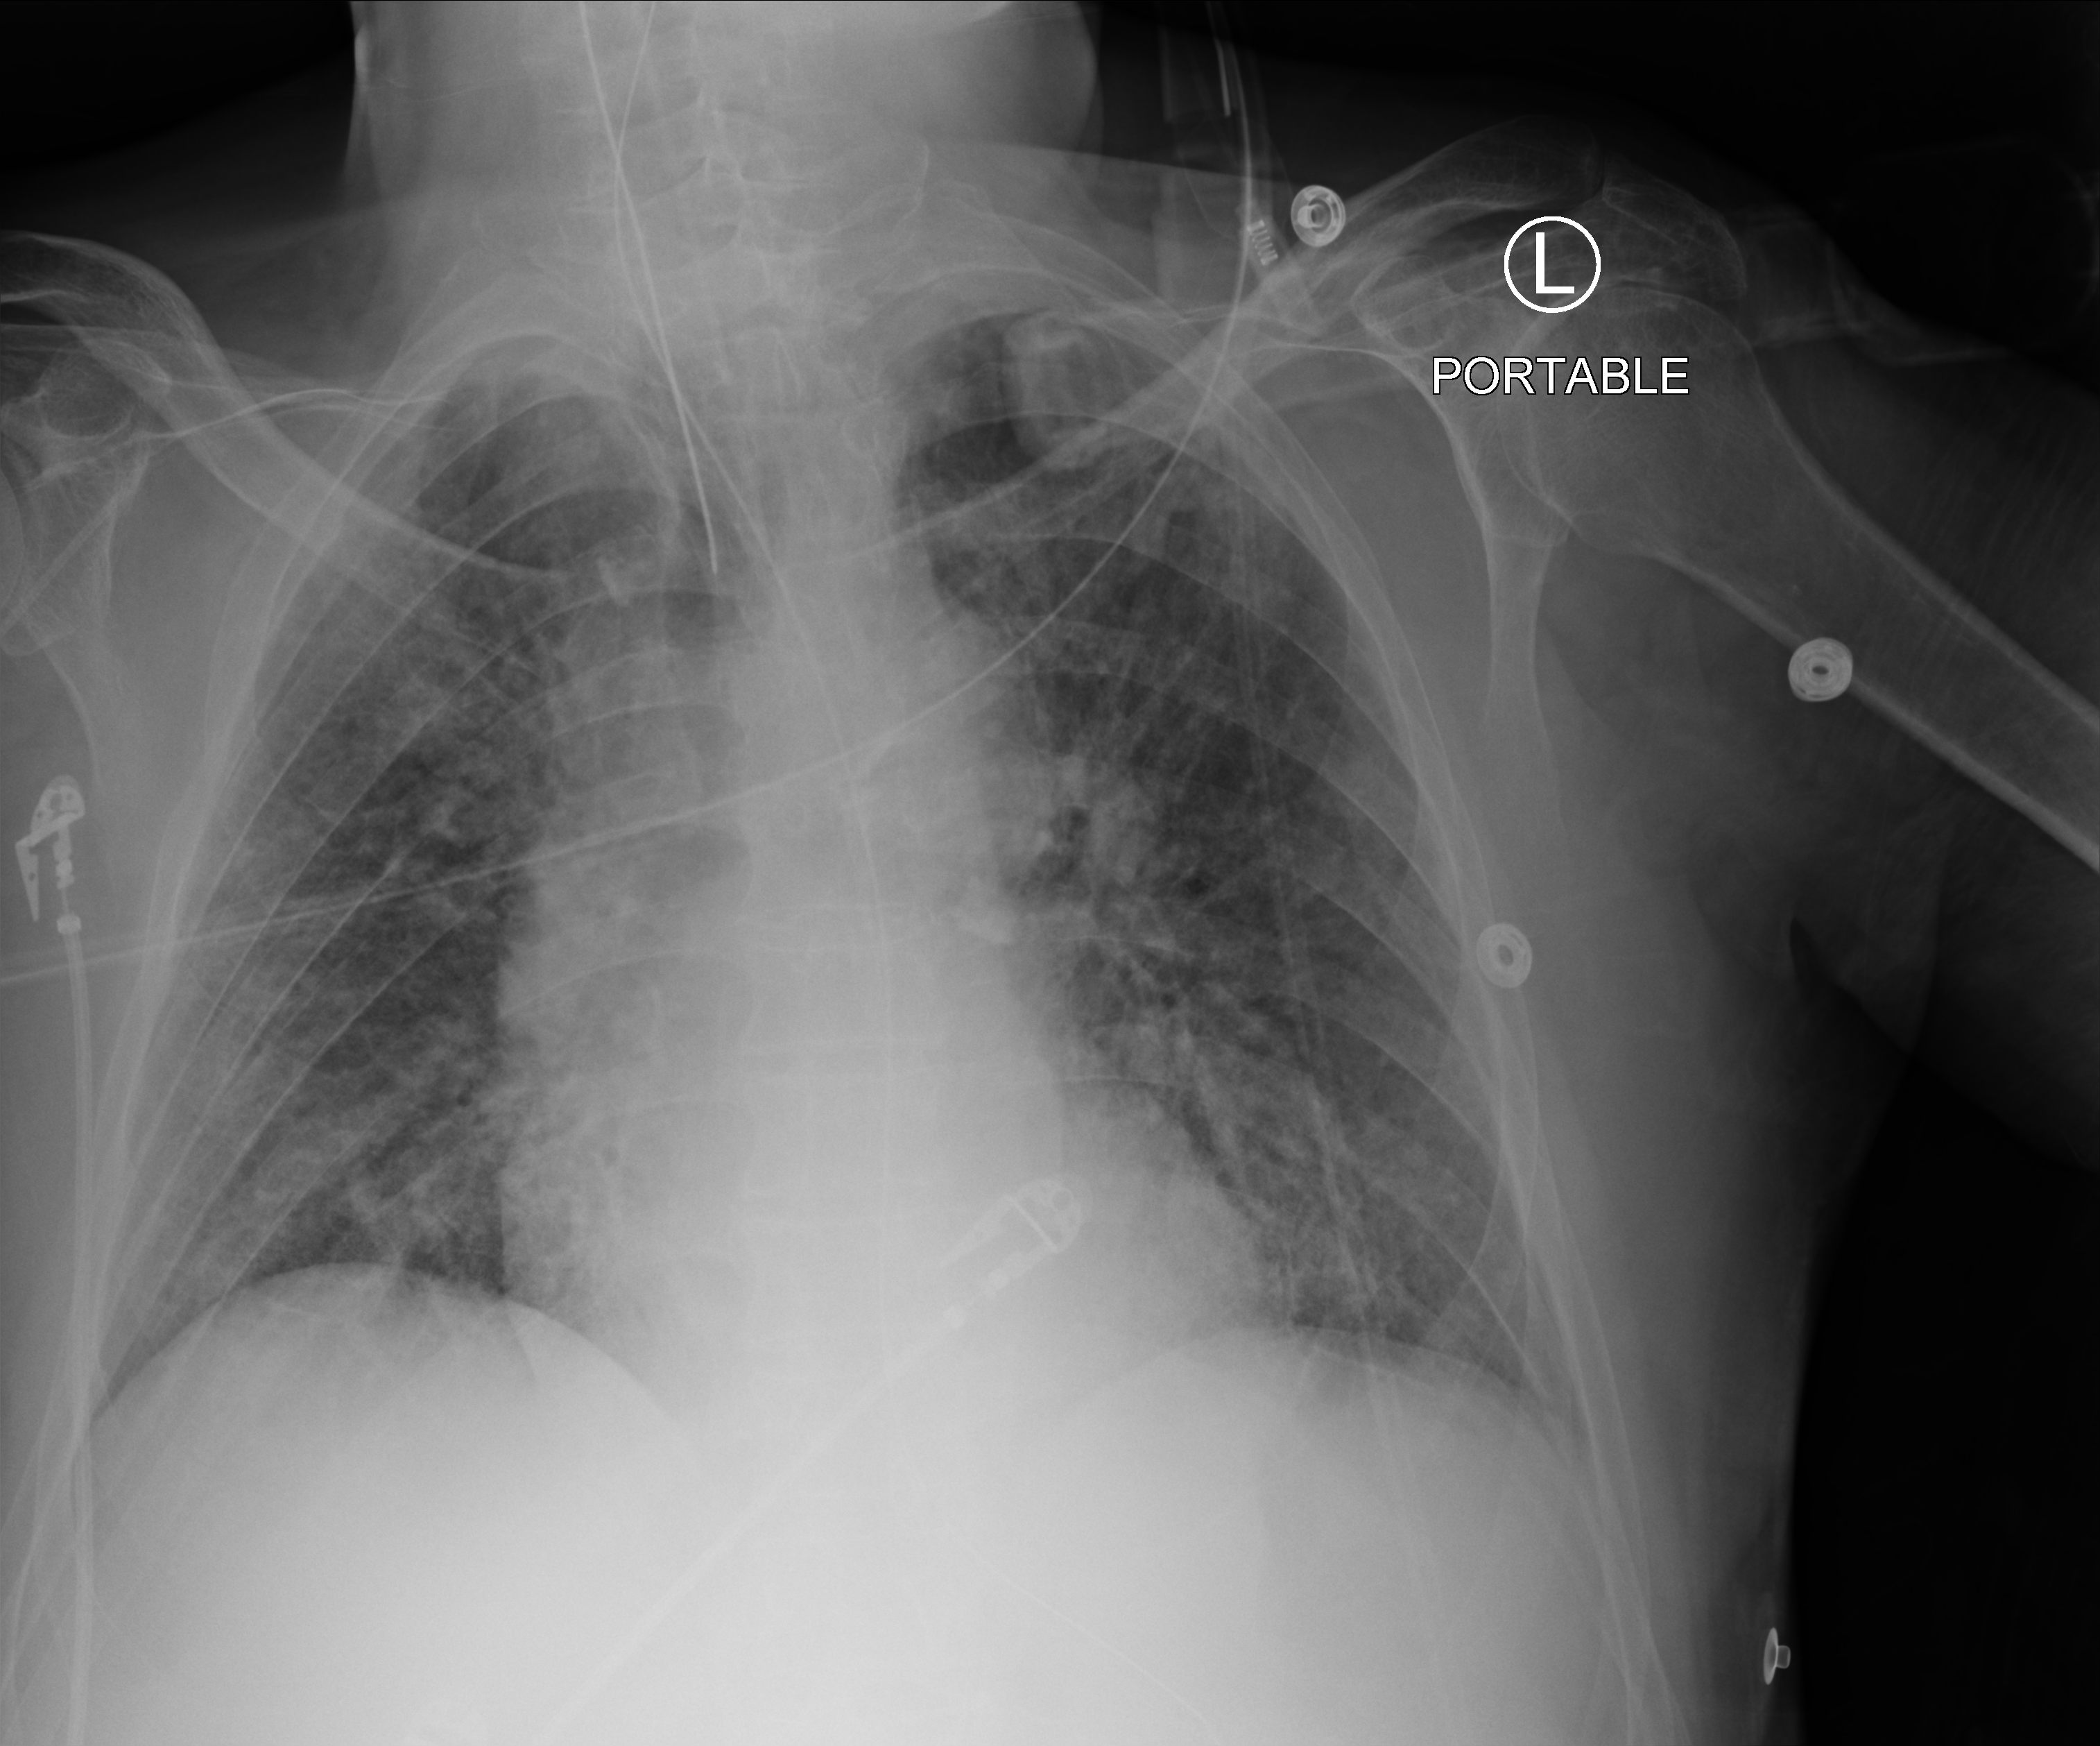
Portable chest radiograph. Male patient hospitalised with COVID-19, age 60–74 years.
Admission-level facts for this patient (not findings on this image; timing relative to this image not recorded):
- length of hospital stay: 25 days
- other chronic lung disease (admission record): no
- diabetes (admission record): no